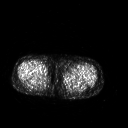
FDG PET of an extremity soft-tissue mass (from a PET/CT study), one axial slice. Slice 223 of 267 in the series (ordered by position). 3.27 mm slice thickness. 128 × 128 image matrix, field of view 500 × 500 mm. Patient: female, 42 years. From the clinical record (not read from this slice): histological type: pleiomorphic leiomyosarcoma; grade: intermediate; site of the primary tumour: left thigh.
Structures marked on this image (expert contour drawn on MRI and transferred to this co-registered scan by the dataset authors):
- gross tumour volume including surrounding oedema: bounding box [x1, y1, x2, y2] px = [65, 72, 81, 79]